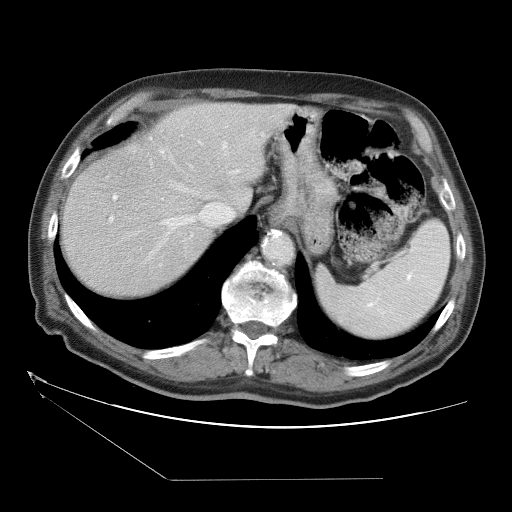
Contrast-enhanced abdominal CT (liver protocol), one axial slice. Slice 27 of 38 in the series (ordered by position). One of 2 acquisitions stored at this slice position. Soft-tissue window (W 400 / L 40 HU). 512 × 512 image matrix, field of view 400 × 400 mm. Case-level facts recorded for this patient, not image findings: diagnosis: hepatocellular carcinoma (patient treated with transarterial chemoembolisation; whether this scan precedes or follows treatment is not stated here); TNM stage (as recorded): Stage-II; Child-Pugh class: A; tumour differentiation: moderately differentiated.
Outlined on this slice (semi-automatic segmentation, software-assisted and operator-edited):
- abdominal aorta: box from (x=263, y=236) to (x=292, y=263) px
- liver parenchyma outside the tumour (the mass and vessels are separate outlines, so this box may not span the whole liver): (x=62, y=102)–(x=316, y=294)
- liver vessels: (x=108, y=141)–(x=229, y=266)